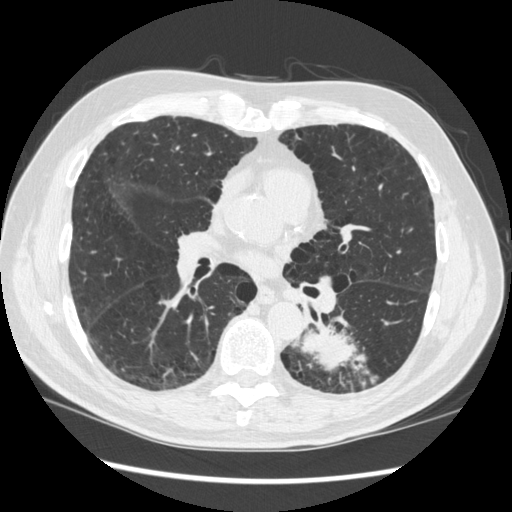
Chest CT (low-dose screening protocol), one axial image, first (baseline) screen, lung window (W 1500 / L -600 HU), slice 165 of 348 in the series. Male participant, aged 72 years at enrolment. Current smoker at enrolment.
Lesion marked by an expert reader, bounding box (x1, y1, x2, y2) in pixels: (264, 306, 368, 399). The screening reader recorded 2 non-calcified nodules or masses ≥4 mm on this exam; which of them this box marks is not recorded. Official screen result: positive, change unspecified: nodule(s) >= 4 mm or enlarging nodule(s), mass(es), or other non-specific abnormalities suspicious for lung cancer.